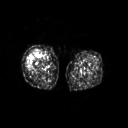
FDG PET of an extremity soft-tissue mass (from a PET/CT study), one axial slice; position 220 of 311 along the scan axis; 3.27 mm slice thickness; 128 × 128 image matrix, field of view 500 × 500 mm. Patient: female, 57 years. Case-level facts recorded for this patient, not image findings: histological type: pleiomorphic undifferentiated sarcoma; grade: high; site of the primary tumour: right quadricep.
Outlined on this slice (expert contour drawn on MRI and transferred to this co-registered scan by the dataset authors):
- tumour plus oedema (research contour): bounding box (x1, y1, x2, y2) in pixels: (26, 51, 41, 67)